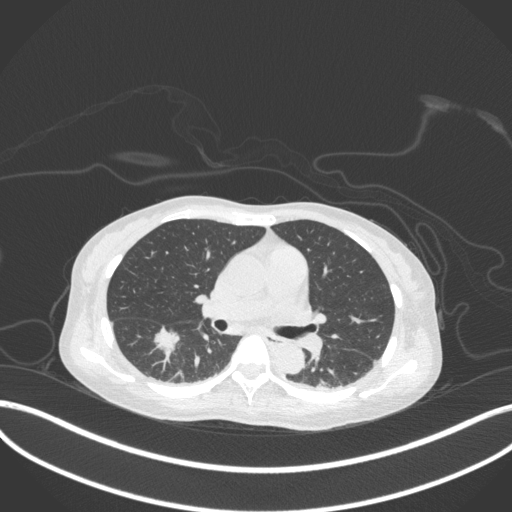
Chest CT, one axial slice; position 174 of 260 along the scan axis; 120 kVp; lung window (W 1500 / L -600 HU); 1 mm slice thickness; 512 × 512 image matrix, field of view 400 × 400 mm. Patient: female, 44 years. From the clinical record (not read from this slice): clinical TNM (as recorded): T1c N0 M0.
Structures marked on this image (bounding box drawn by a radiologist):
- lung tumour (recorded histology: adenocarcinoma): bounding box <151,322,180,359> (left, top, right, bottom; pixels)